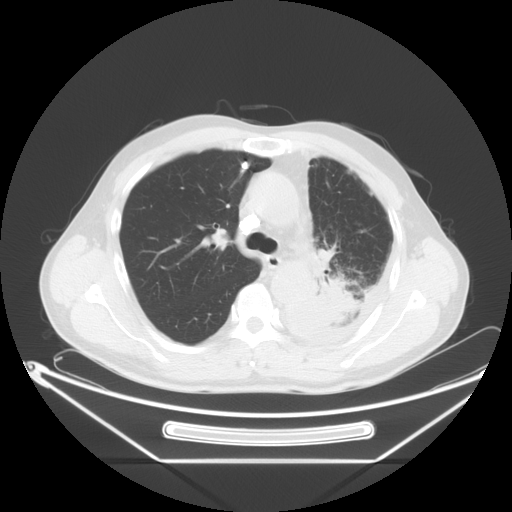
Chest CT, one axial slice. Slice 42 of 63 in the series (ordered by position). Reconstruction kernel STANDARD. Lung window (W 1500 / L -600 HU). 512 × 512 image matrix, field of view 442 × 442 mm. Male patient, age 60 years. Case-level facts recorded for this patient, not image findings: clinical TNM (as recorded): T4 N1 M1.
Structures marked on this image (bounding box drawn by a radiologist):
- lung tumour (recorded histology: adenocarcinoma): bounding box <301,254,372,336> (left, top, right, bottom; pixels)